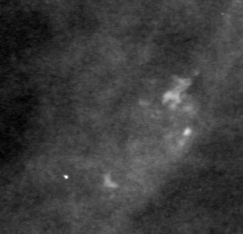
Cropped region of a digitized screen-film mammogram centred on a radiologist-marked abnormality, left breast, MLO view.
- Finding: calcifications, morphology pleomorphic, distribution clustered; BI-RADS assessment category 4; pathology result (as recorded, not read from the image): benign.